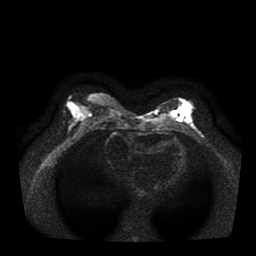
Breast MRI, one axial slice; diffusion-weighted series; image 2 of 4 stored at this slice position (different b-values; order by instance number); 1.5 T; 256 × 256 image matrix, field of view 330 × 330 mm. Female patient.
Outlined on this slice (outlined manually by an expert reader):
- tumour on diffusion-weighted imaging: box from (x=177, y=108) to (x=183, y=115) px